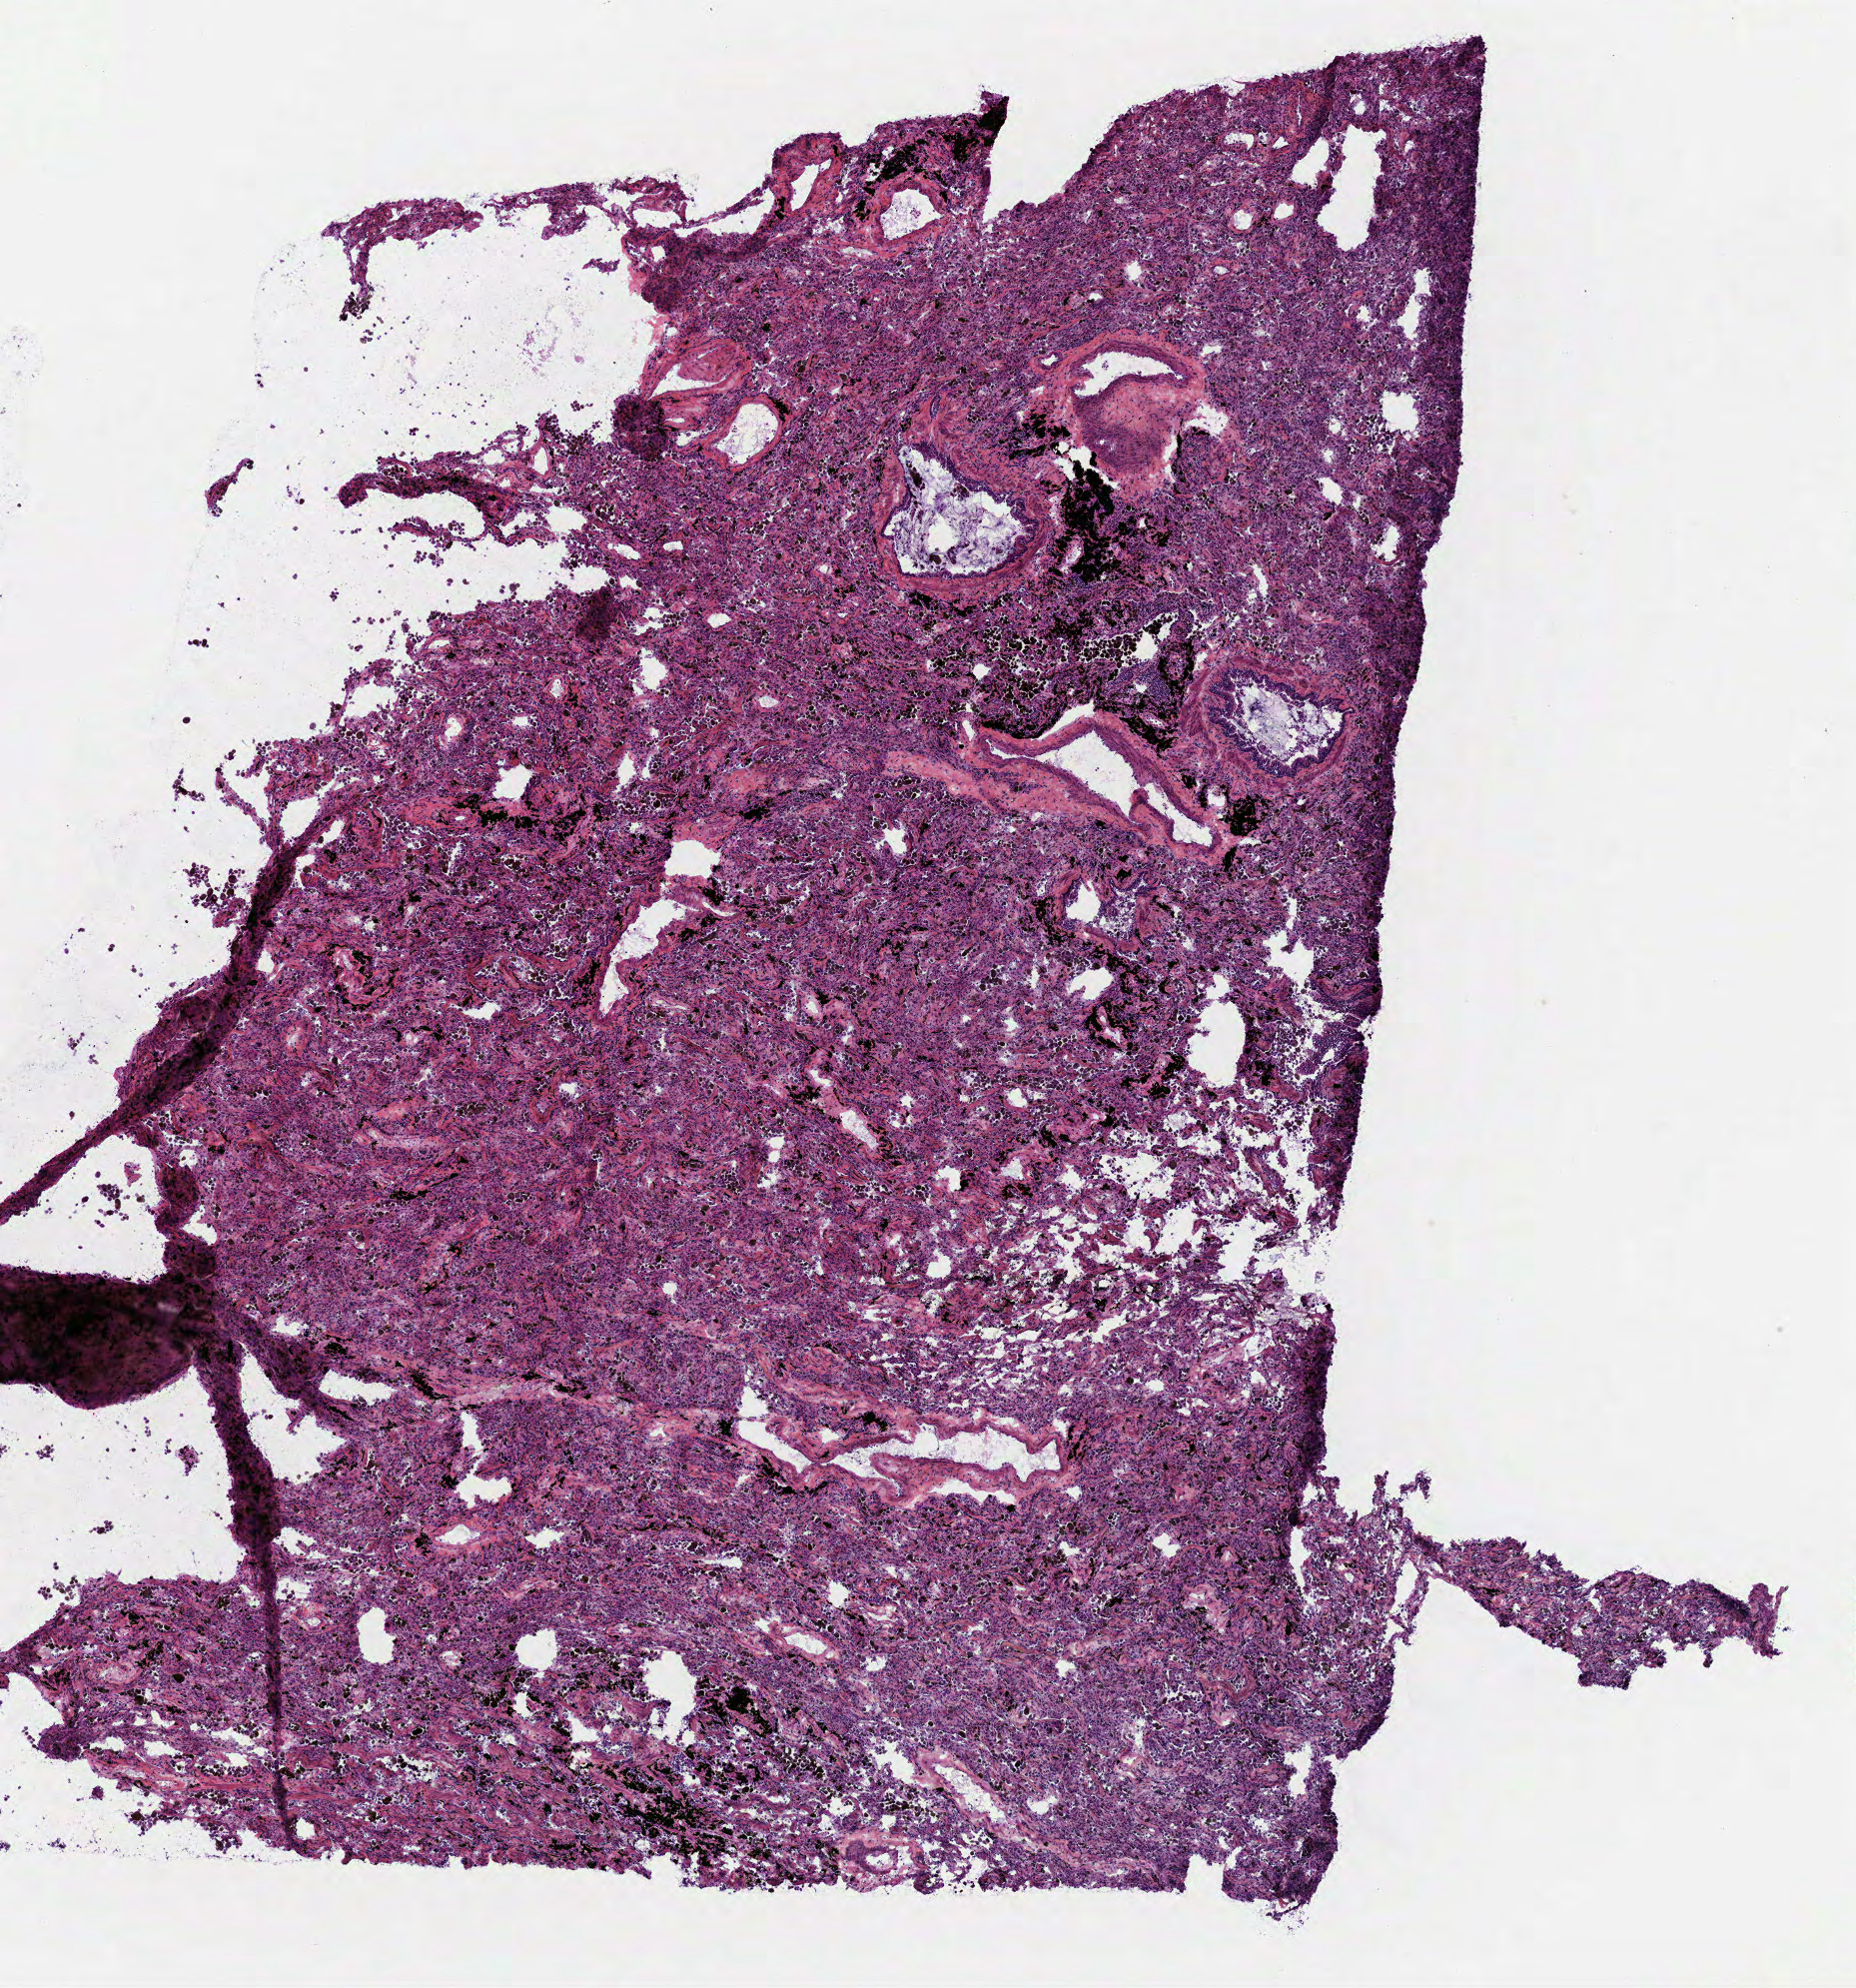
Digitized H&E tissue section (whole slide), a low-resolution overview of the entire scanned area, about 7.5 x 8.0 mm (acquisition: 40x scan); frozen section; lung, solid tissue normal (non-tumour tissue) sample. Female, age 50 years at initial diagnosis.
This section: solid tissue normal (non-tumour) sample from the same patient. Patient diagnosis: Adenocarcinoma, NOS (lower lobe, lung).